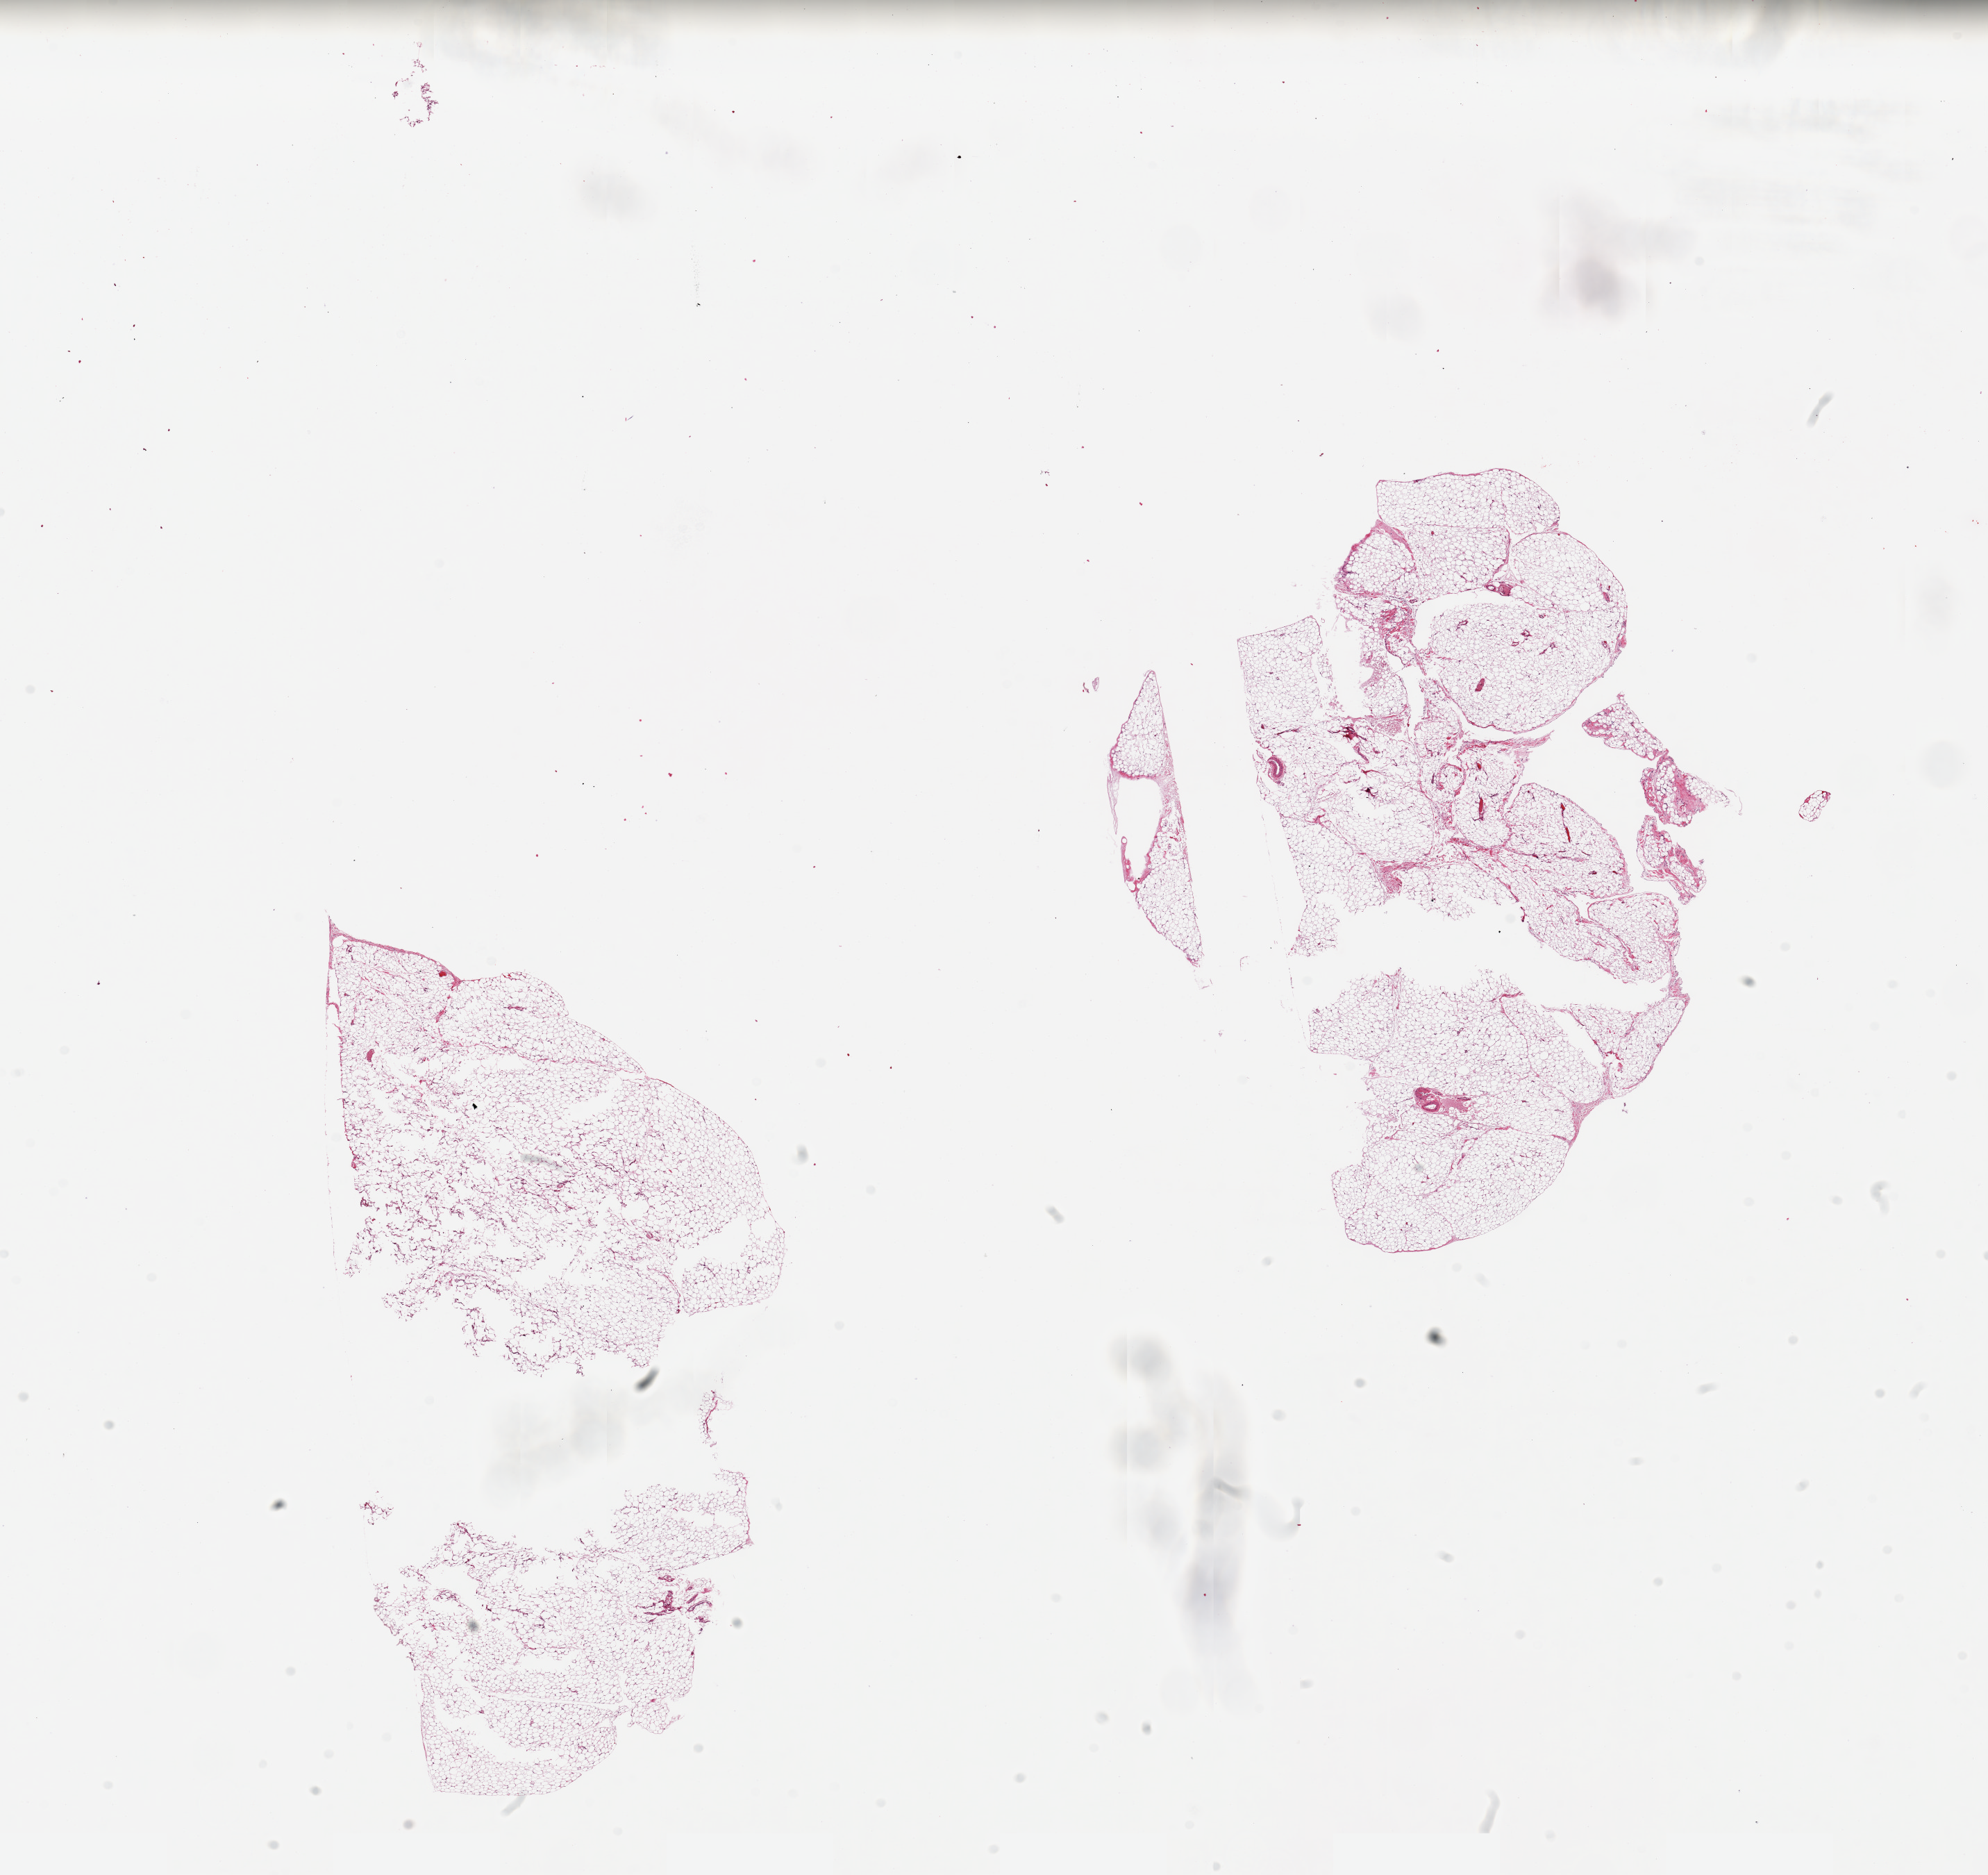
Whole-slide image, haematoxylin and eosin stain, shown as a low-resolution overview of the whole scanned area (about 22.6 x 21.4 mm, slide scanned at 20x); PAXgene-fixed paraffin-embedded (PFPE) section; section of omentum (target tissue); tissue donor sample. Male donor.
Reviewer comment on this tissue sample: 2 pieces, 10x6 & 8x5.5mm; Artefactual fractures.